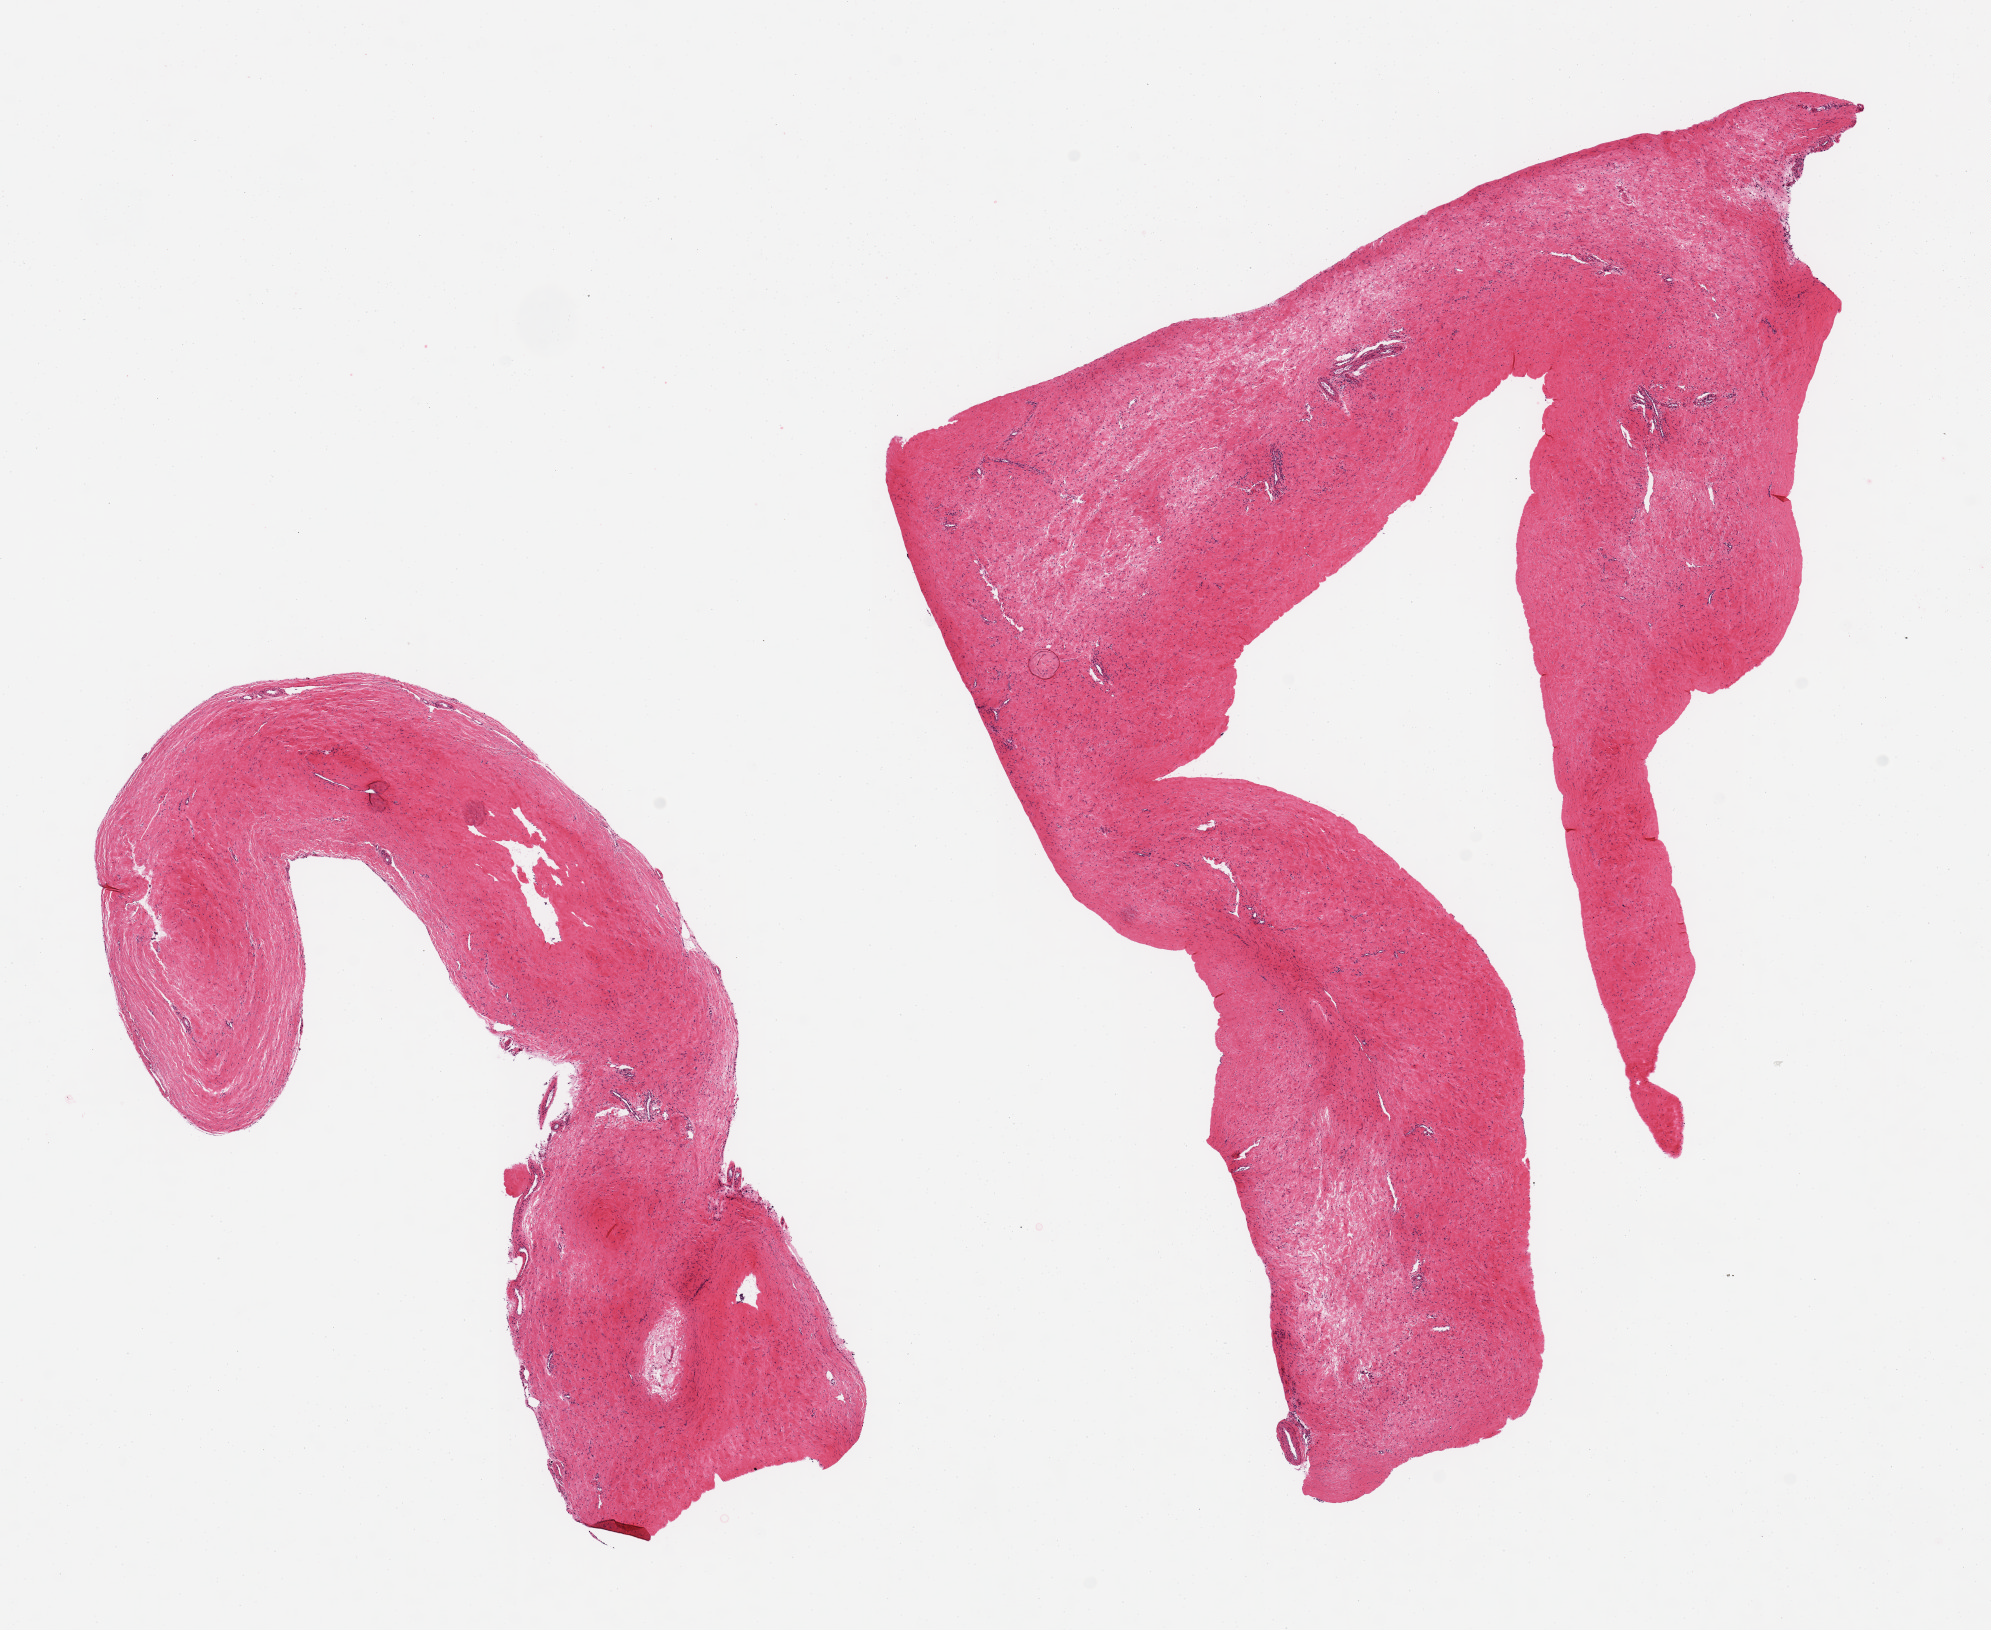
Whole-slide image, H&E stain, a low-resolution overview of the entire scanned area, about 15.8 x 12.9 mm (acquisition: 20x scan). PAXgene-fixed, paraffin-embedded tissue. Sampled site (target tissue): testis. Tissue donor sample.
Pathologist's review note for this sample: 2 pieces. Not testis. Stromal tissue of unknown provenance.